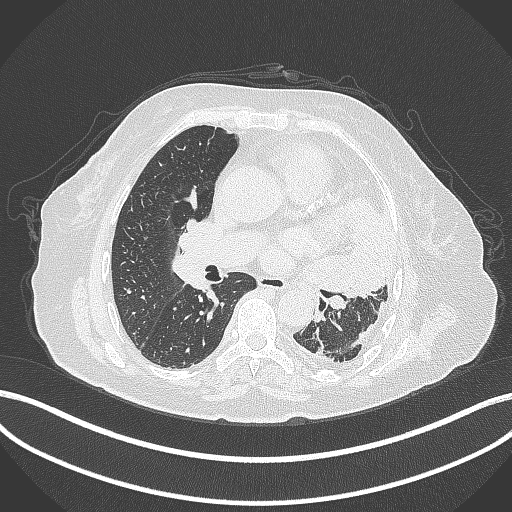
Chest CT, one axial slice; position 194 of 399 along the scan axis; reconstruction kernel B70f; lung window (W 1500 / L -600 HU); 1 mm slice thickness; 512 × 512 image matrix. Patient: female, 75 years. Case-level facts recorded for this patient, not image findings: clinical TNM (as recorded): T3 N3 M1.
Outlined on this slice (rectangle marked by the reading radiologist):
- lung tumour (recorded histology: adenocarcinoma): bounding box (x1, y1, x2, y2) in pixels: (310, 190, 408, 307)